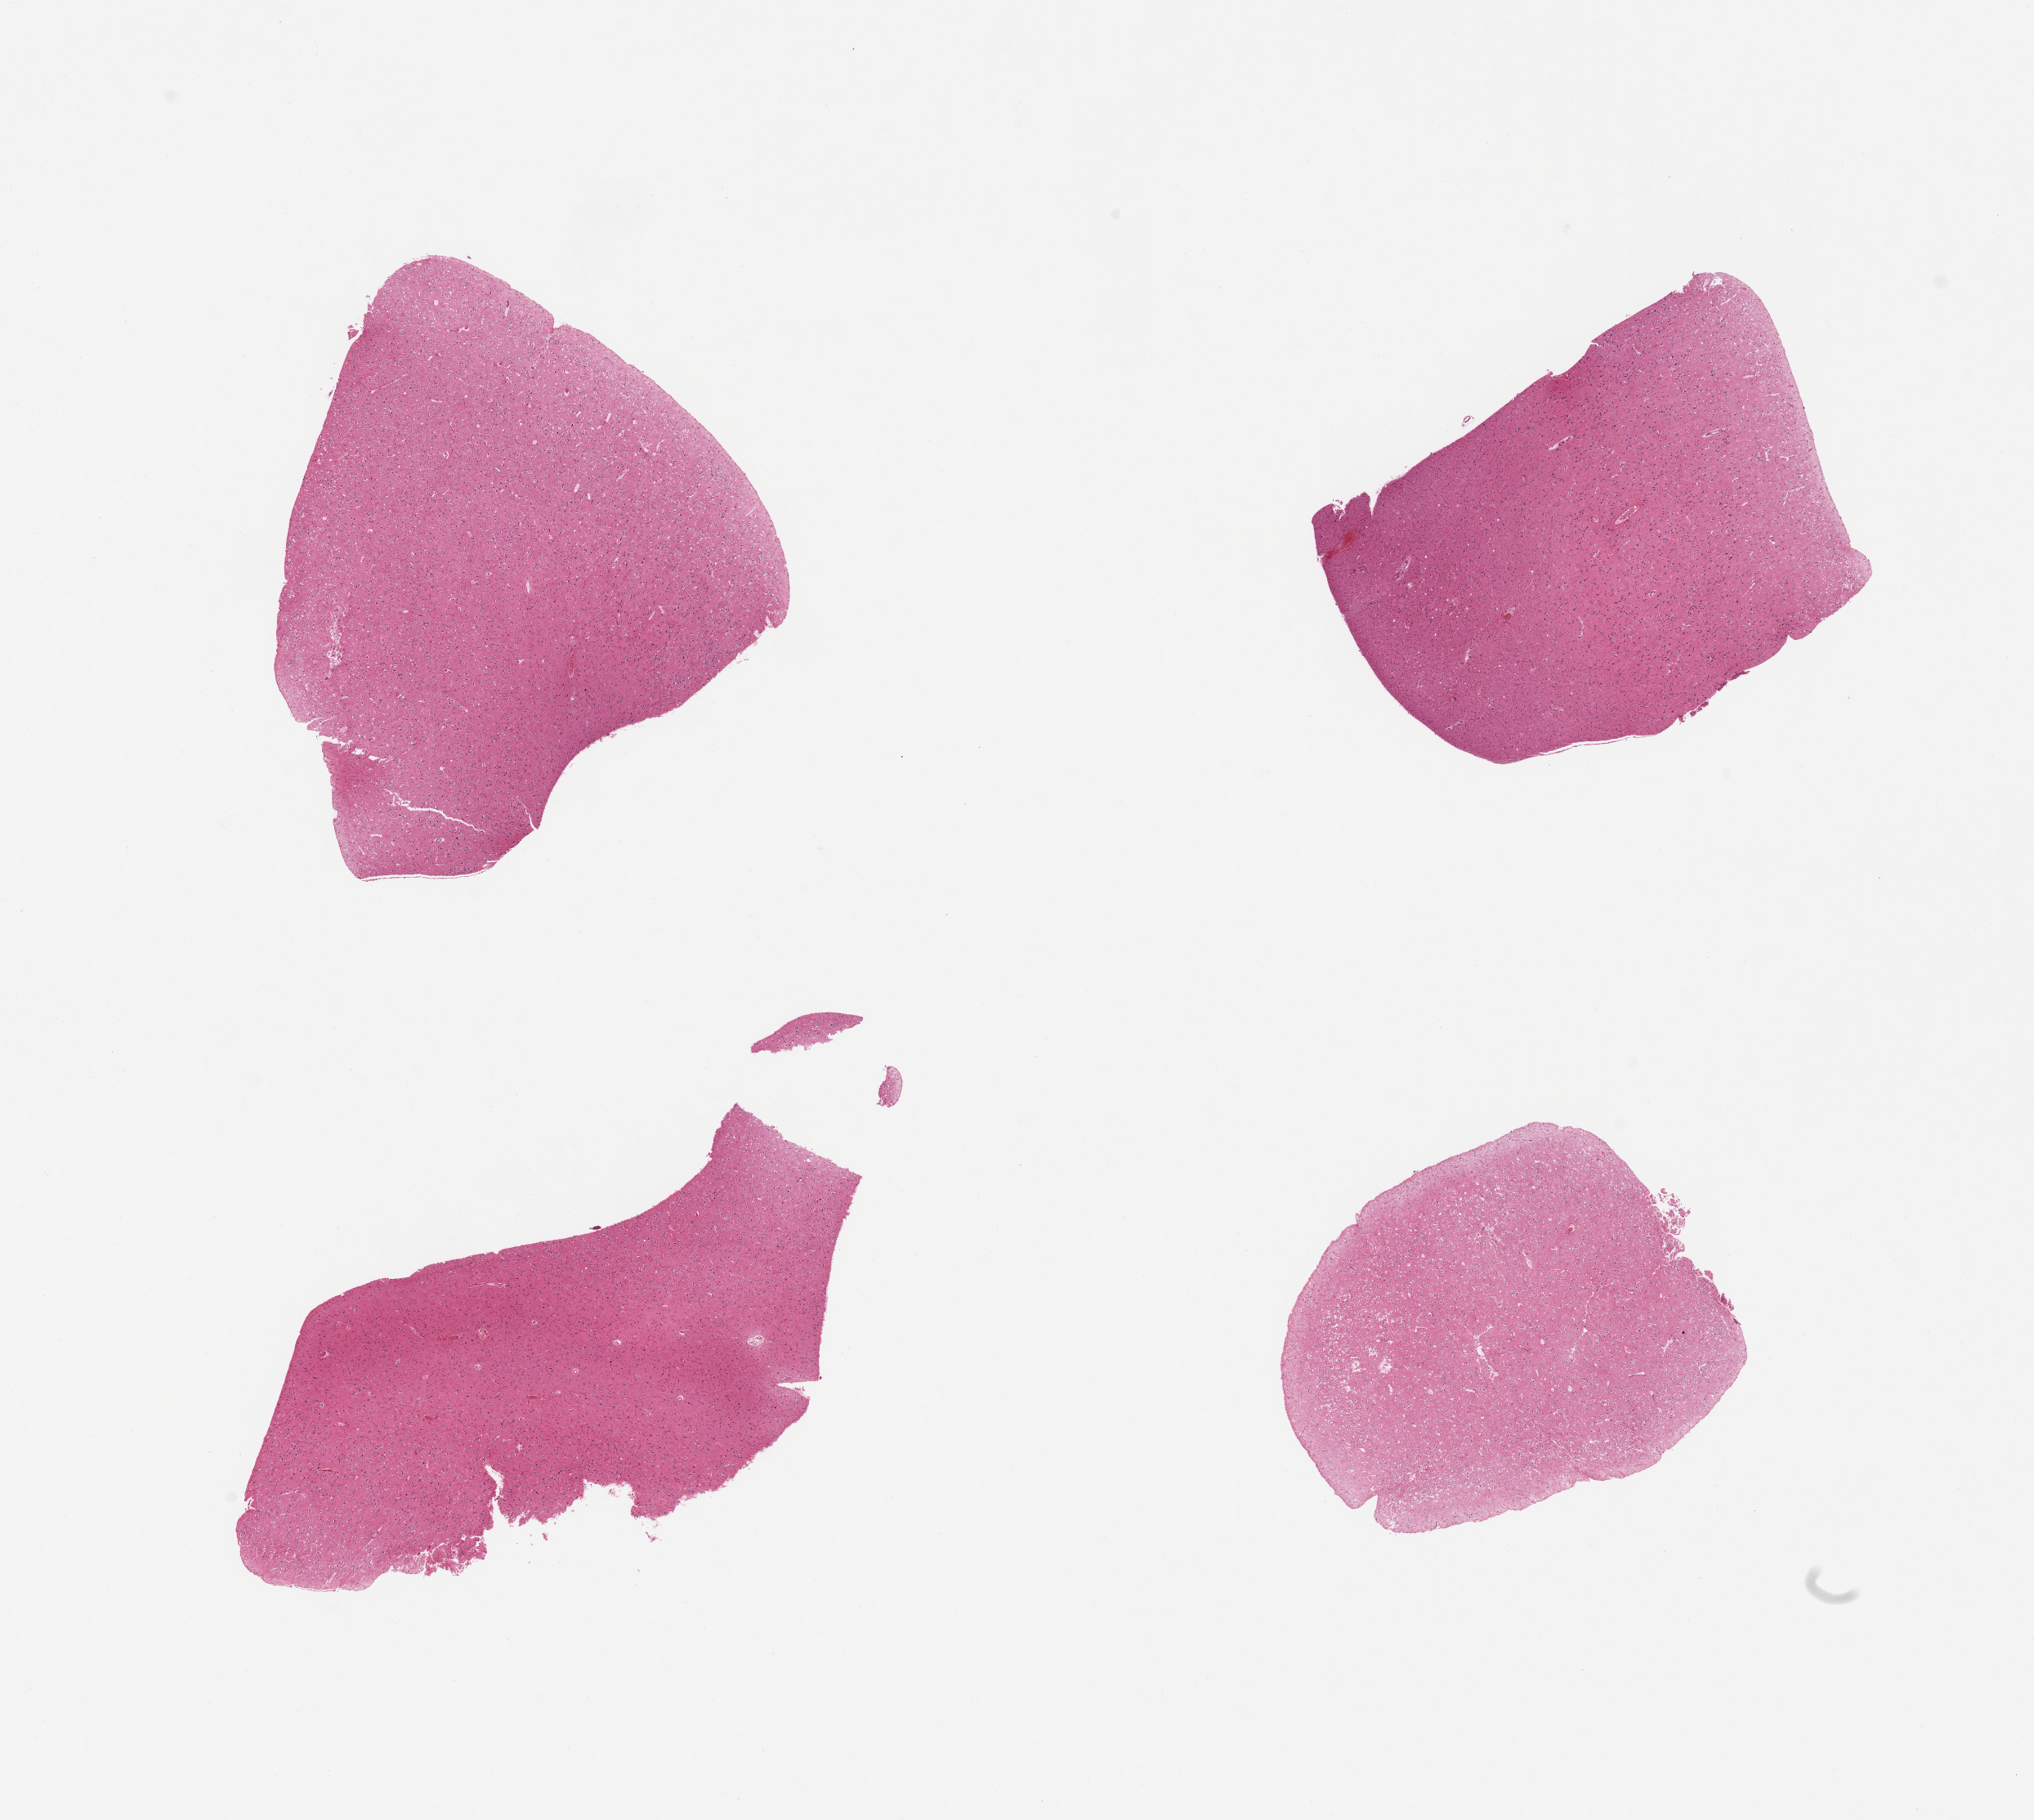
Digitized H&E-stained section, brightfield, whole scanned area (about 19.7 x 17.6 mm) shown as a low-resolution overview. PAXgene-fixed paraffin-embedded (PFPE) section. Sampled site (target tissue): cerebral cortex. Tissue donor sample. Female donor.
- pathologist's review note for this sample: 4 pieces